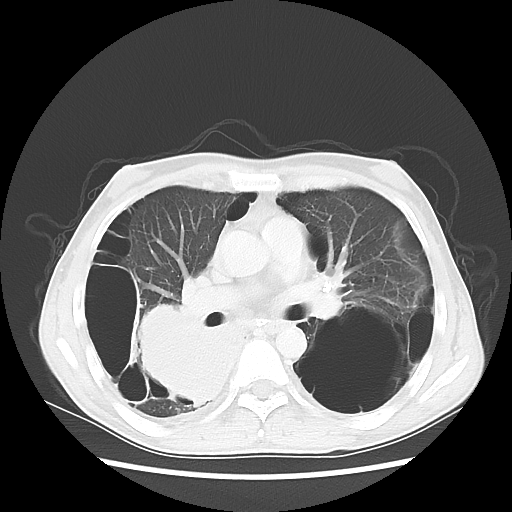
Chest CT, one axial slice. Position 31 of 57 along the scan axis. 140 kVp. Lung window (W 1500 / L -600 HU). 5 mm slice thickness. 512 × 512 image matrix, field of view 351 × 351 mm. Patient: male, 41 years. From the clinical record (not read from this slice): clinical TNM (as recorded): T4 N0 M1a; histopathological grade: G3.
Annotated regions visible in this slice (bounding box drawn by a radiologist):
- lung tumour (recorded histology: large cell carcinoma): box from (x=133, y=298) to (x=252, y=408) px